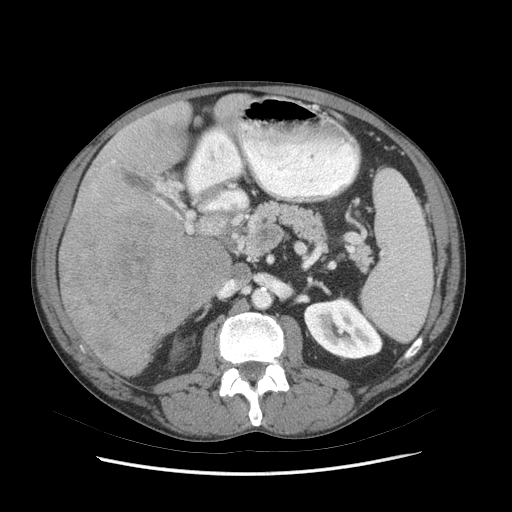
Contrast-enhanced abdominal CT (liver protocol), one axial slice. Position 33 of 89 along the scan axis. Reconstruction kernel STANDARD. Soft-tissue window (W 400 / L 40 HU). 2.5 mm slice thickness. 512 × 512 image matrix, field of view 380 × 380 mm. Case-level facts recorded for this patient, not image findings: diagnosis: hepatocellular carcinoma (patient treated with transarterial chemoembolisation; whether this scan precedes or follows treatment is not stated here); TNM stage (as recorded): Stage-IIIB; Child-Pugh class: A; tumour differentiation: moderately differentiated; tumour nodularity: multinodular.
Outlined on this slice (semi-automatic segmentation, software-assisted and operator-edited):
- liver parenchyma outside the tumour (the mass and vessels are separate outlines, so this box may not span the whole liver): box from (x=58, y=94) to (x=250, y=376) px
- mass: (x=60, y=205)–(x=236, y=375)
- liver vessels: (x=112, y=160)–(x=211, y=231)